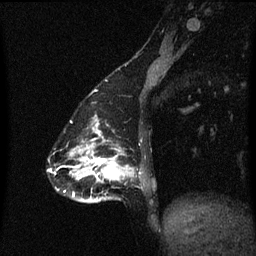
Breast MRI (dynamic contrast-enhanced), one sagittal slice. Slice 17 of 60 in the series (ordered by position). Dynamic contrast-enhanced series, image 2 of 3 at this slice position (ordered by acquisition). 1.5 T. TE 4.2 ms, TR 8.4 ms. 2 mm slice thickness. 256 × 256 image matrix, field of view 200 × 200 mm. Patient: female, 47 years.
Annotated regions visible in this slice (semi-automatically segmented with operator editing):
- analysis volume of interest (the breast-tissue region the enhancement analysis was run in; not a lesion): bounding box [x1, y1, x2, y2] px = [81, 138, 144, 203]
- tumour enhancement mask (voxels above the 70 % enhancement threshold inside the analysis volume of interest): [81, 138, 134, 183]